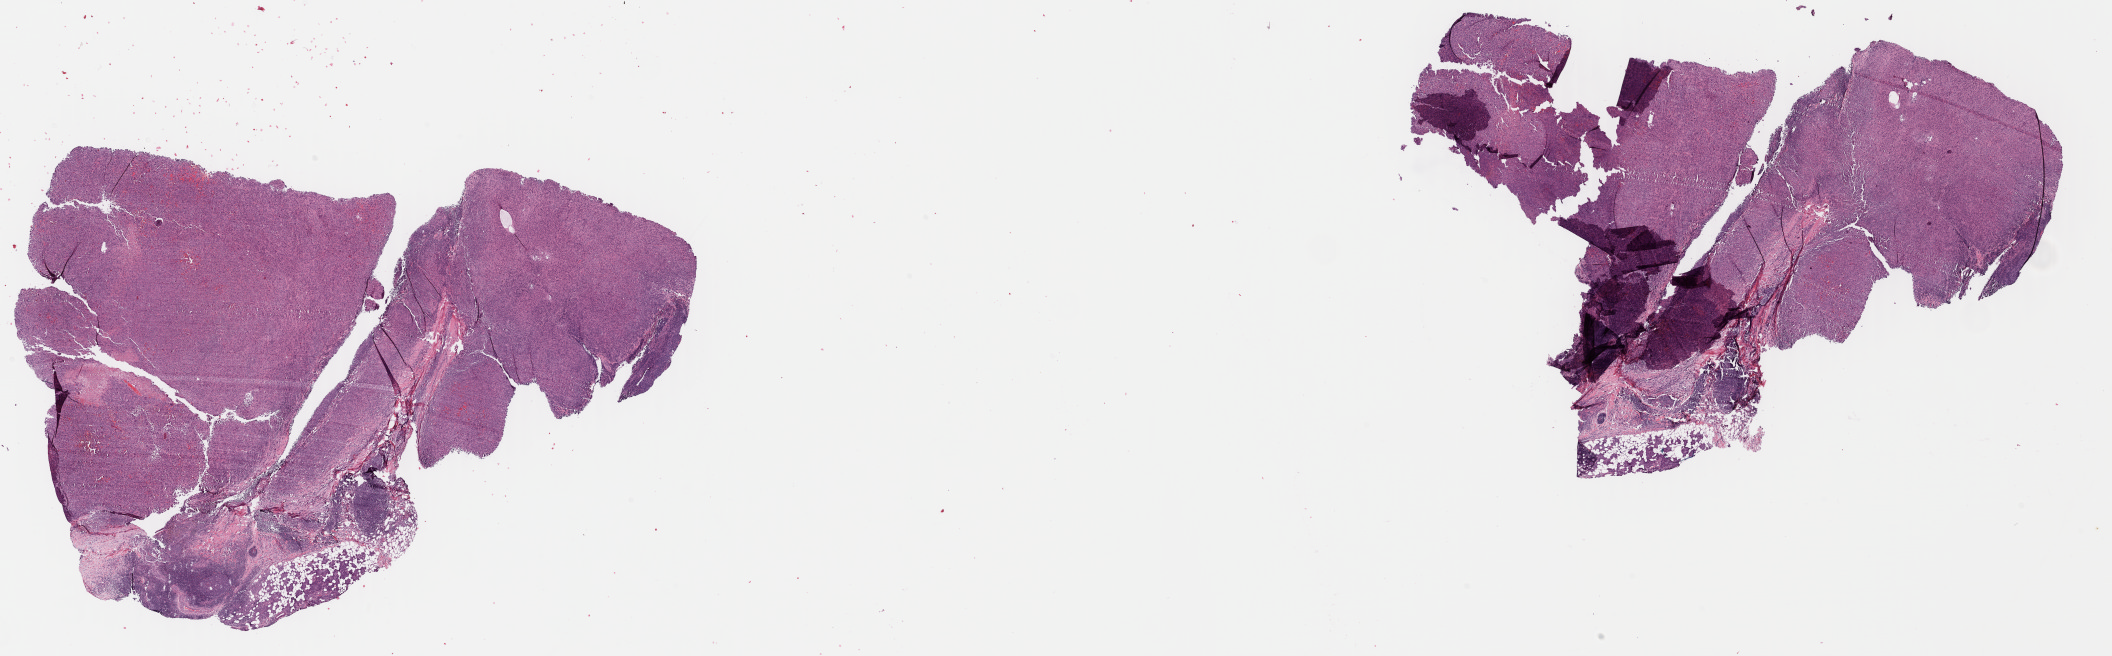
Digitized Hematoxylin and eosin (H&E) stained tissue section (whole slide) — whole scanned area (about 33.2 x 10.3 mm, acquisition: 40x scan) shown as a low-resolution overview; formalin-fixed paraffin-embedded (FFPE) diagnostic section; metastatic tumour sample, sampled site: parotid gland. Male patient; age at initial diagnosis 78 years.
This section: metastatic tumour tissue. Patient diagnosis: Malignant melanoma, NOS.